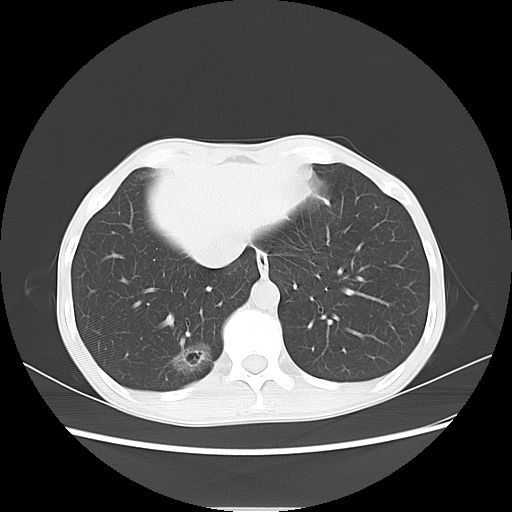
Chest CT, one axial slice. Slice 19 of 69 in the series (ordered by position). Reconstruction kernel LUNG. 120 kVp. Lung window (W 1500 / L -600 HU). 5 mm slice thickness. 512 × 512 image matrix, field of view 350 × 350 mm. Female patient, age 51 years. Case-level facts recorded for this patient, not image findings: clinical TNM (as recorded): T1c N0 M0.
Outlined on this slice (bounding box drawn by a radiologist):
- lung tumour (recorded histology: adenocarcinoma): box from (x=166, y=335) to (x=217, y=384) px